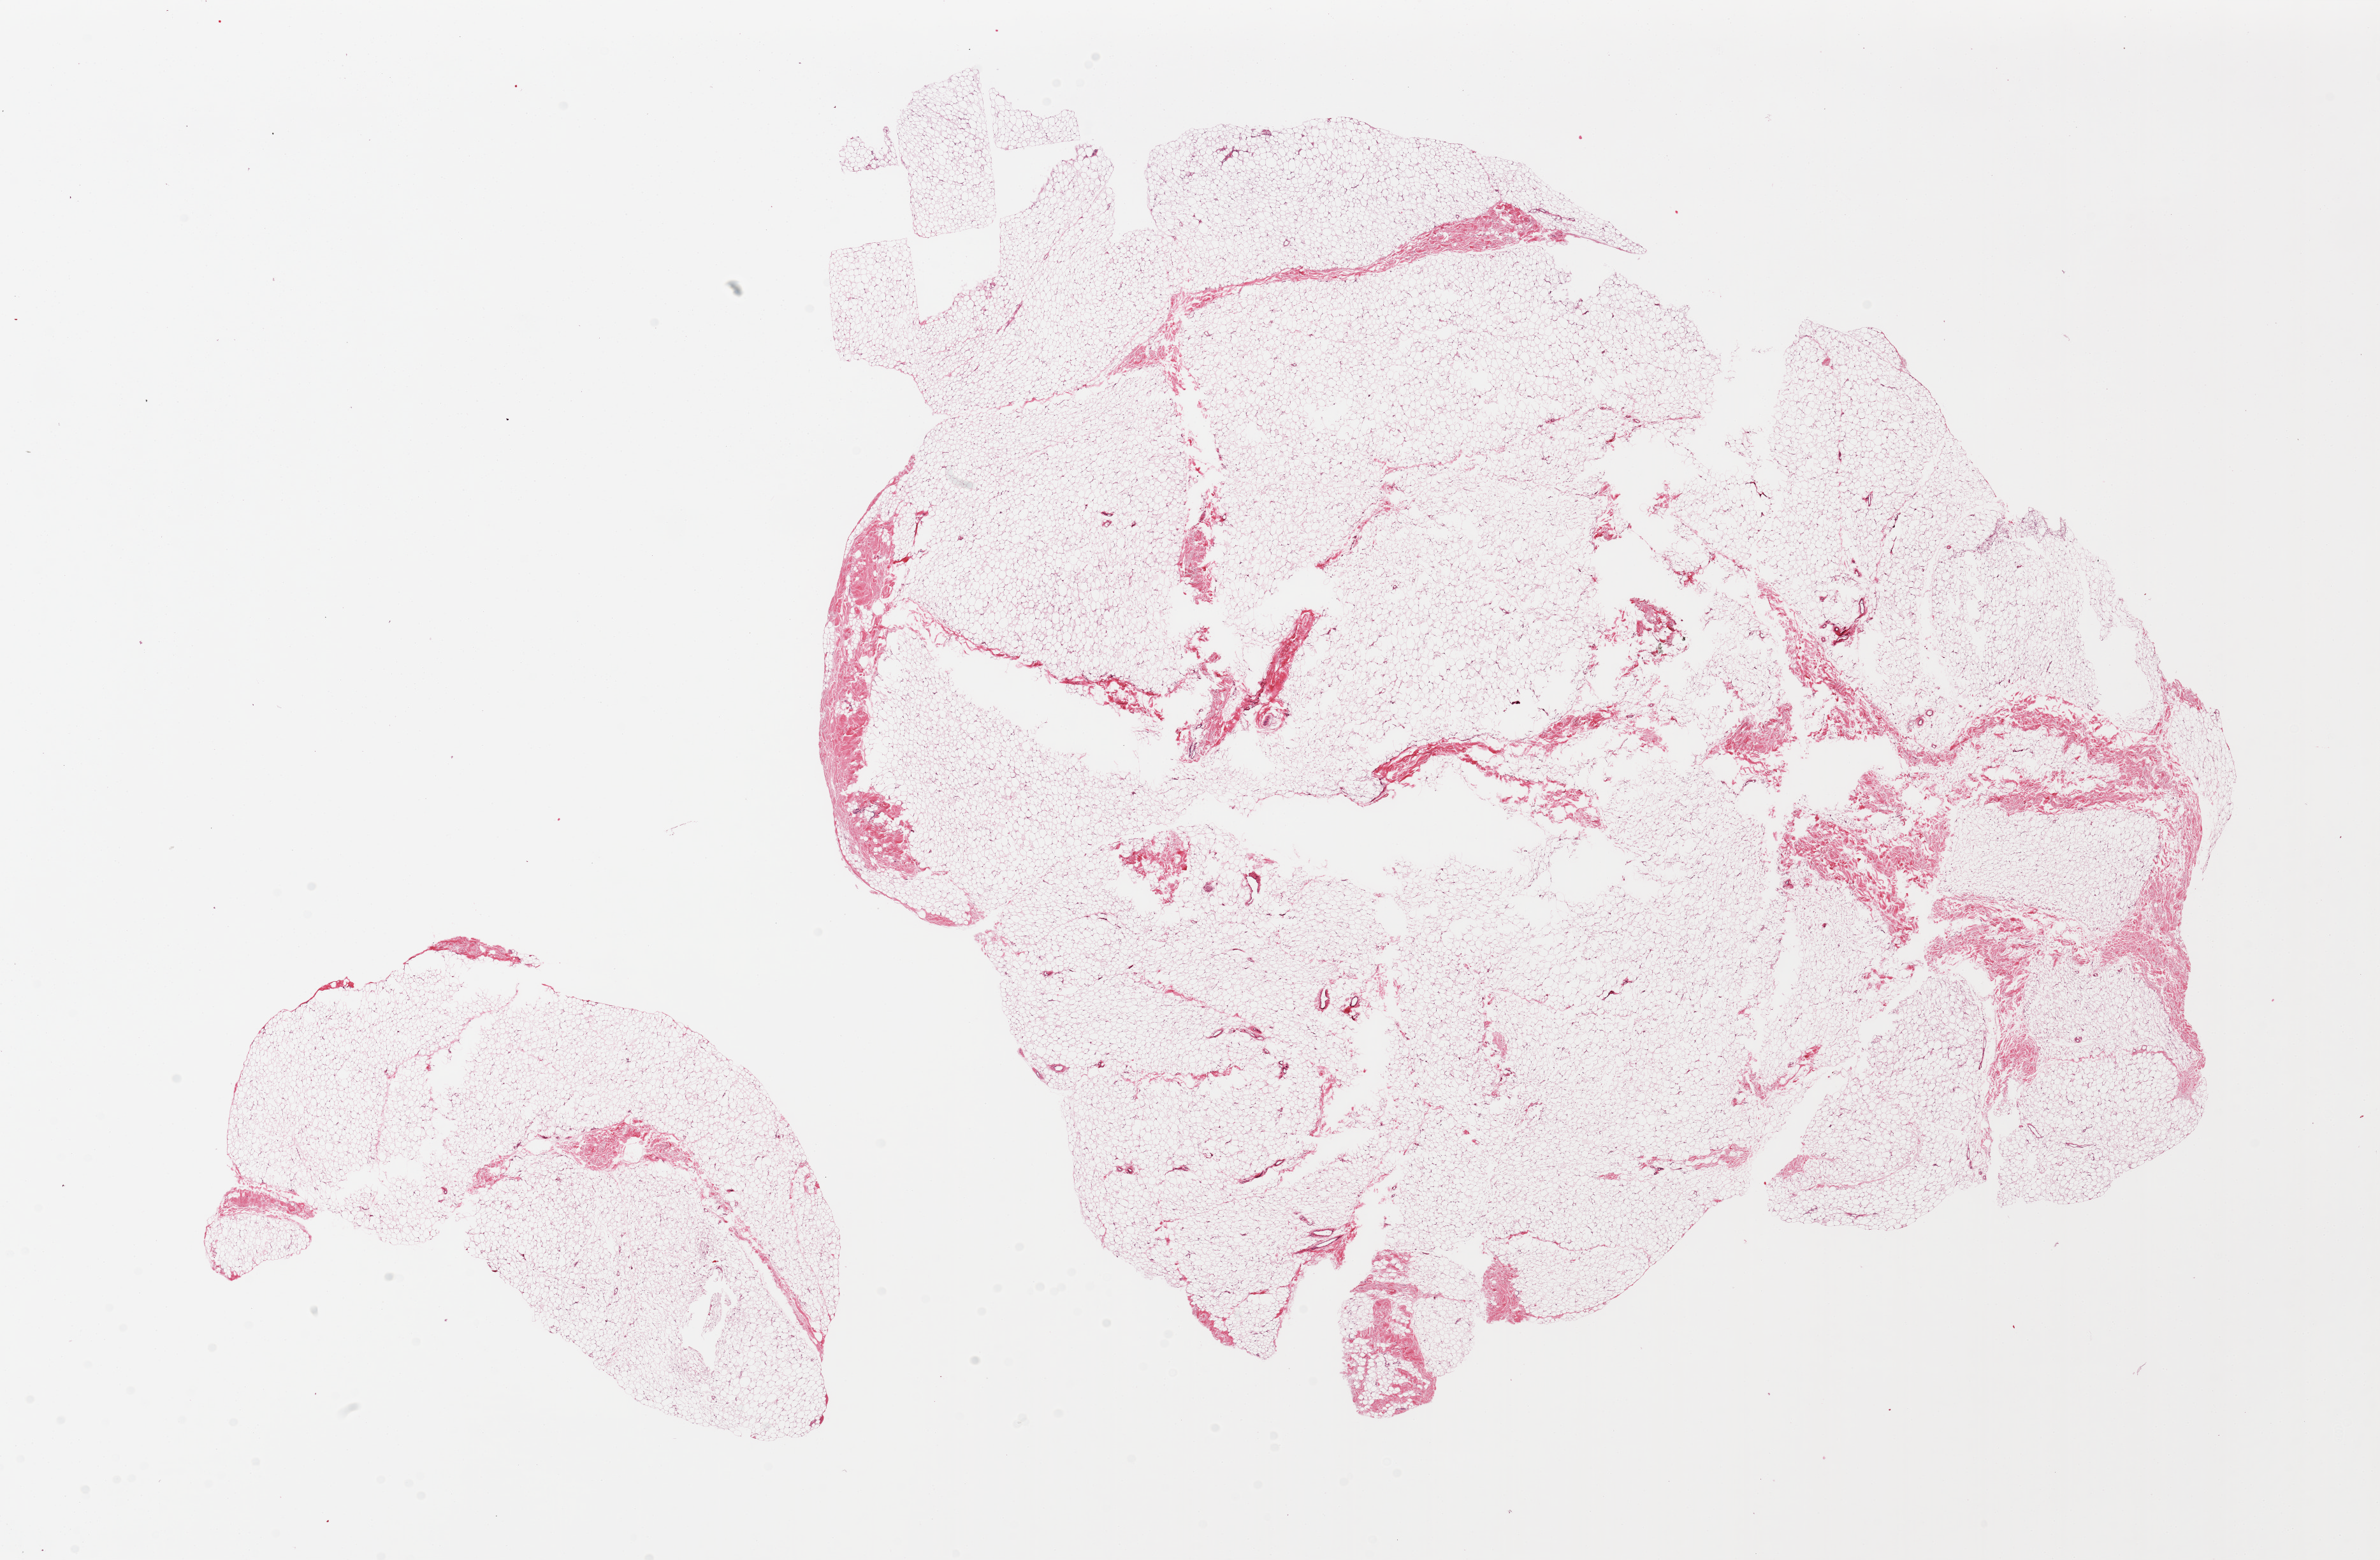
Whole-slide image, H&E stain, shown as a low-resolution overview of the whole scanned area (about 29.5 x 19.4 mm, from a 20x scan); PAXgene-fixed, paraffin-embedded tissue; target tissue: breast; donor tissue sample.
Reviewer comment on this tissue sample: 2 pieces. One overly large piece with central holes. No ducts. Adipose tissue with some fibrous bands.